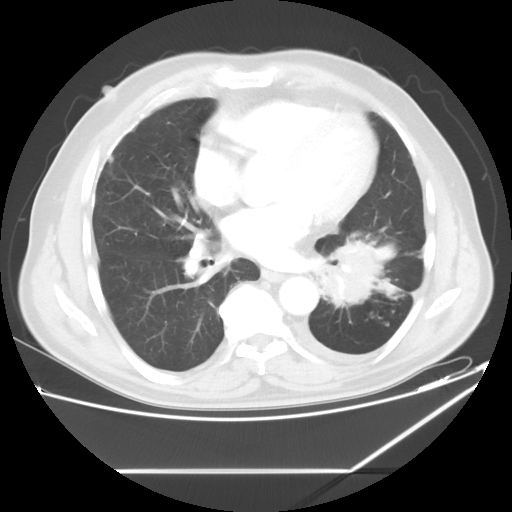
Chest CT, one axial slice. Position 27 of 60 along the scan axis. Reconstruction kernel STANDARD. Lung window (W 1500 / L -600 HU). 512 × 512 image matrix, field of view 395 × 395 mm. Male patient, age 62 years. Case-level facts recorded for this patient, not image findings: clinical TNM (as recorded): T3 N0 M1.
Structures marked on this image (rectangle marked by the reading radiologist):
- lung tumour (recorded histology: adenocarcinoma): bounding box [x1, y1, x2, y2] px = [313, 240, 398, 311]
- lung tumour (recorded histology: adenocarcinoma): [316, 239, 401, 309]